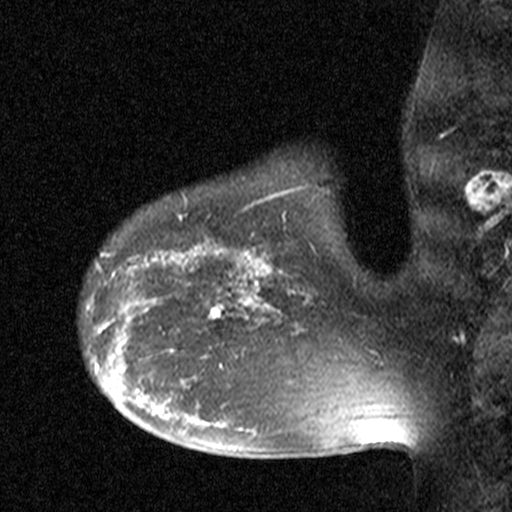
Breast MRI (dynamic contrast-enhanced), one sagittal slice. Slice 34 of 44 in the series (ordered by position). Dynamic contrast-enhanced study with each time point stored as its own series, time point 2 of 3 at this slice position (early post-contrast, ordered by acquisition time). 1.5 T. TE 4.5 ms, TR 11 ms. 3 mm slice thickness. 512 × 512 image matrix. Patient: female, 38 years. From the clinical record (not read from this slice): setting: breast cancer imaged before/during neoadjuvant chemotherapy; receptor status: HR-positive, HER2-negative.
Structures marked on this image (semi-automatic segmentation, software-assisted and operator-edited):
- analysis volume of interest (the breast-tissue region the enhancement analysis was run in; not a lesion): box from (x=176, y=272) to (x=251, y=349) px
- tumour enhancement mask (voxels above the 90 % enhancement threshold inside the analysis volume of interest): (x=207, y=294)–(x=230, y=319)